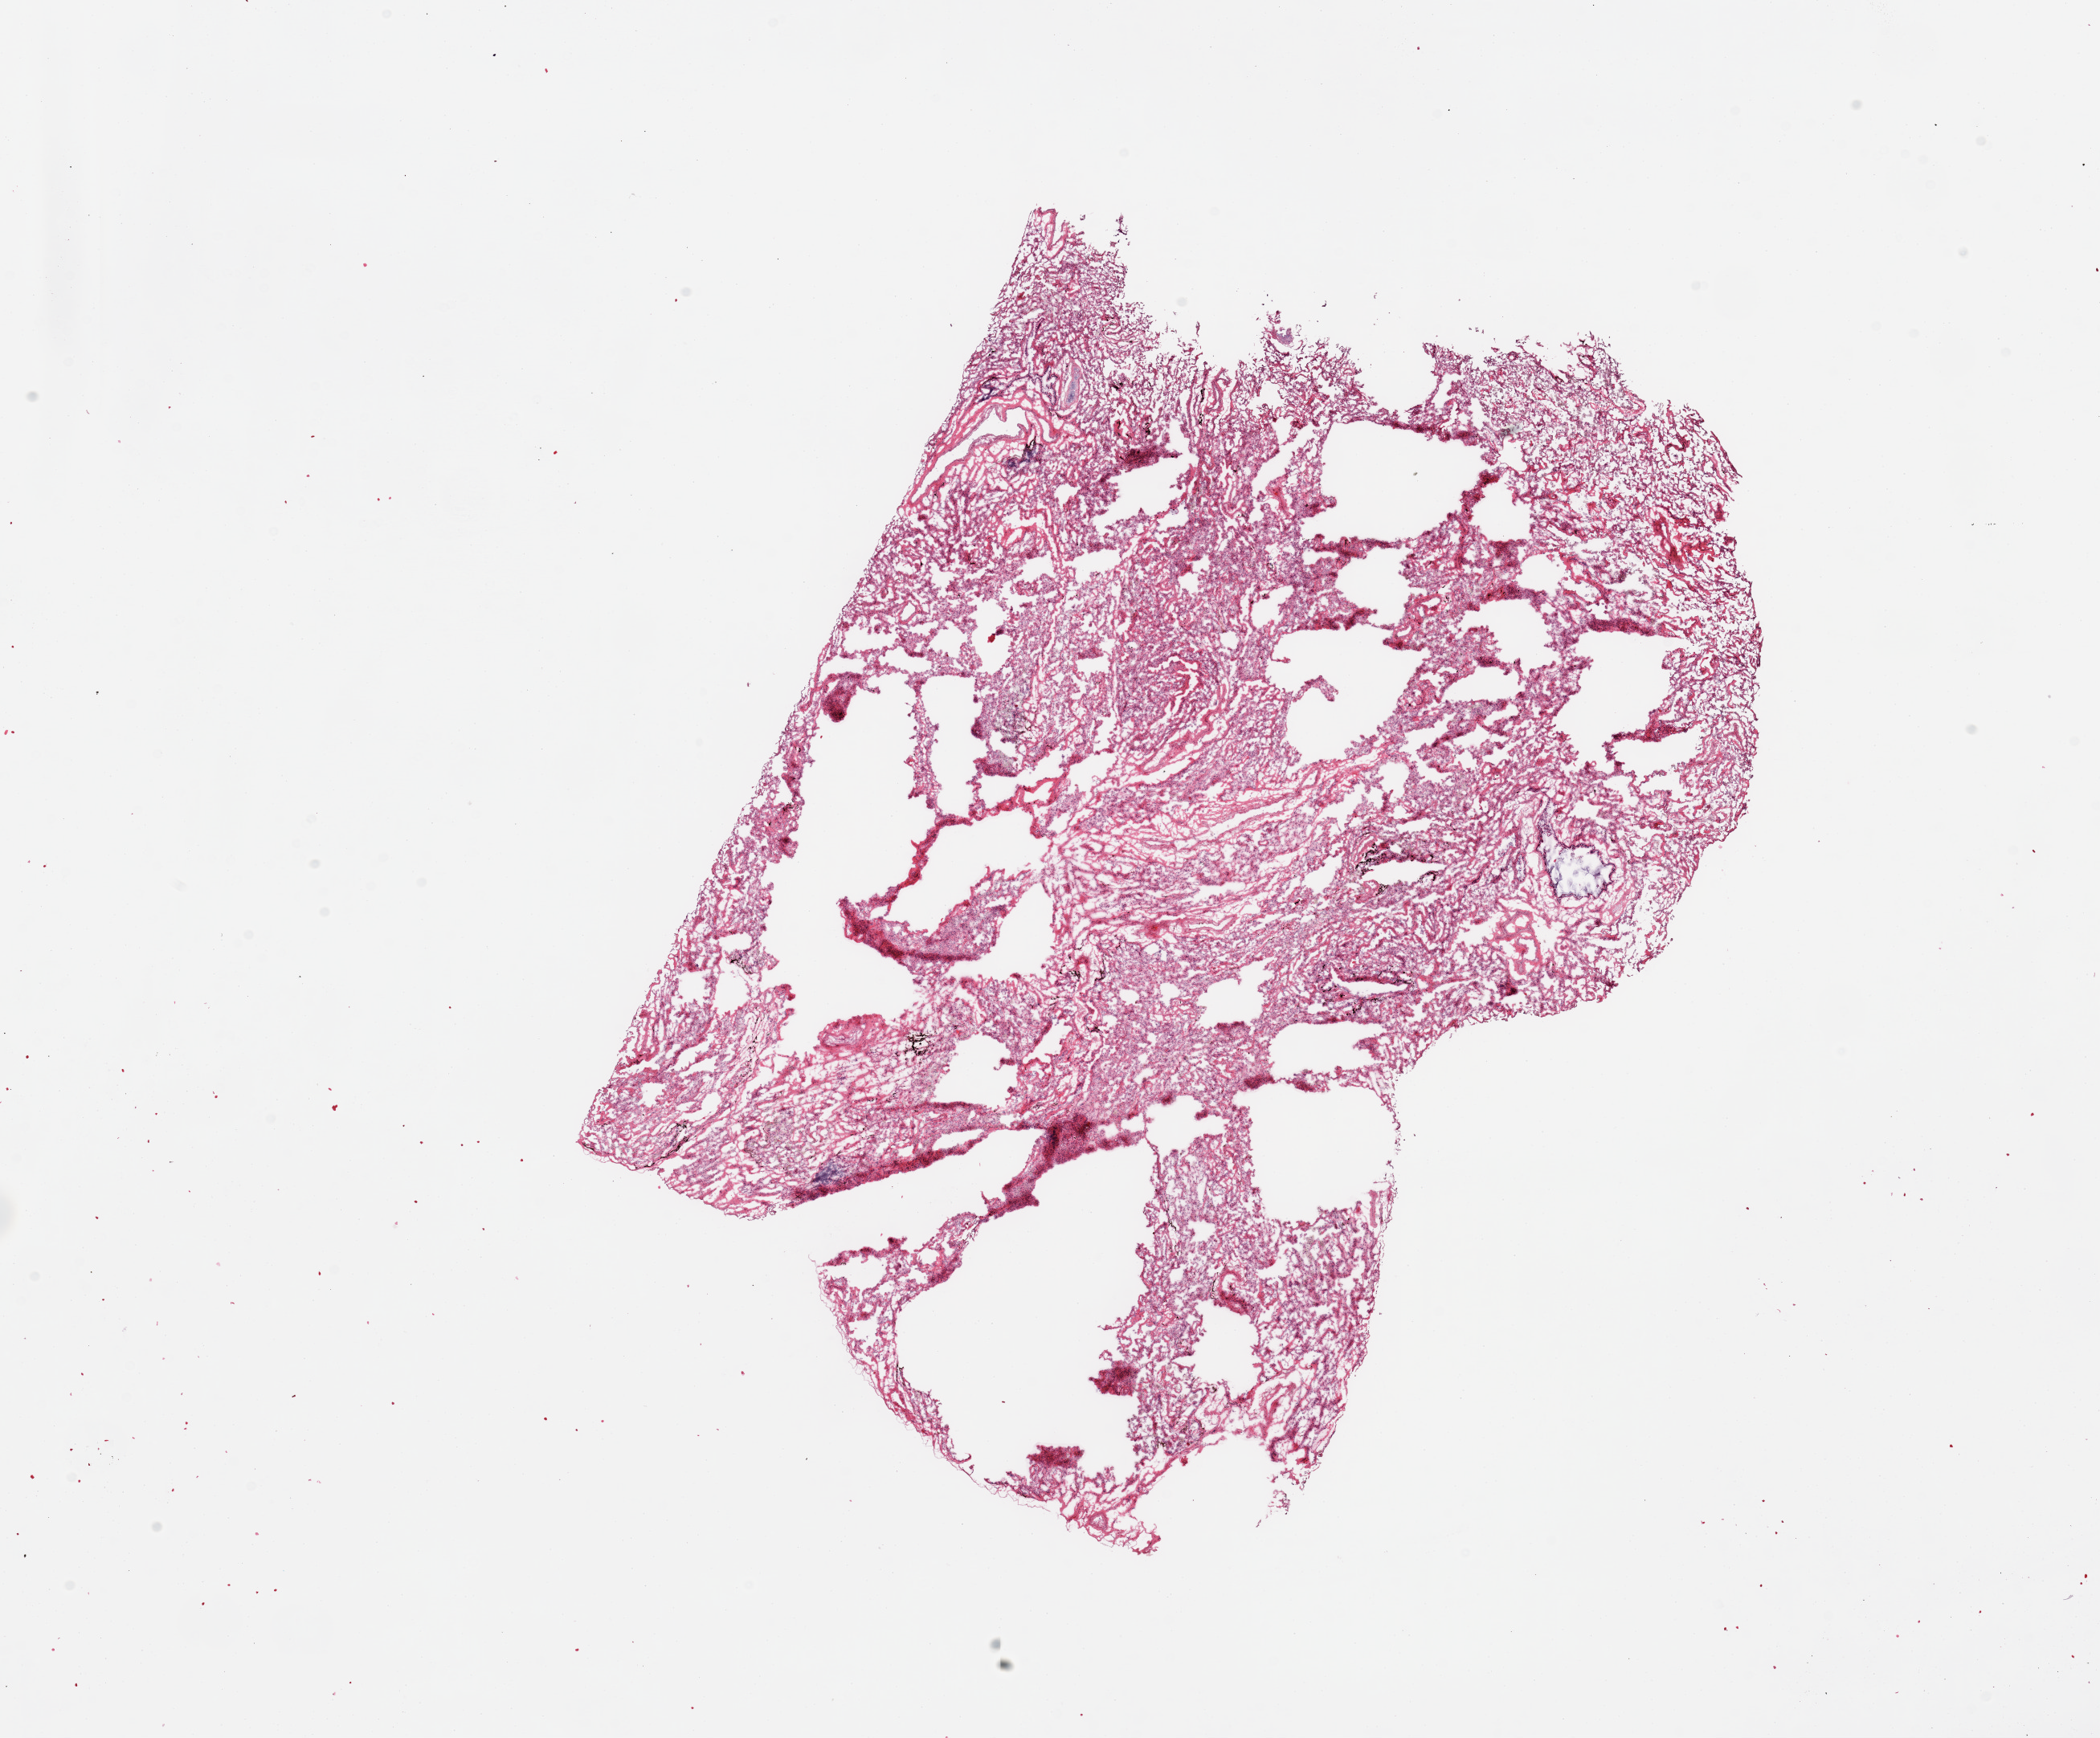
H&E whole-slide image, shown as a low-resolution overview of the whole scanned area (about 20.7 x 17.1 mm, slide scanned at 20x). Donor sex: female.
Specimen: frozen section (dry ice); target tissue: lung; donor tissue sample.